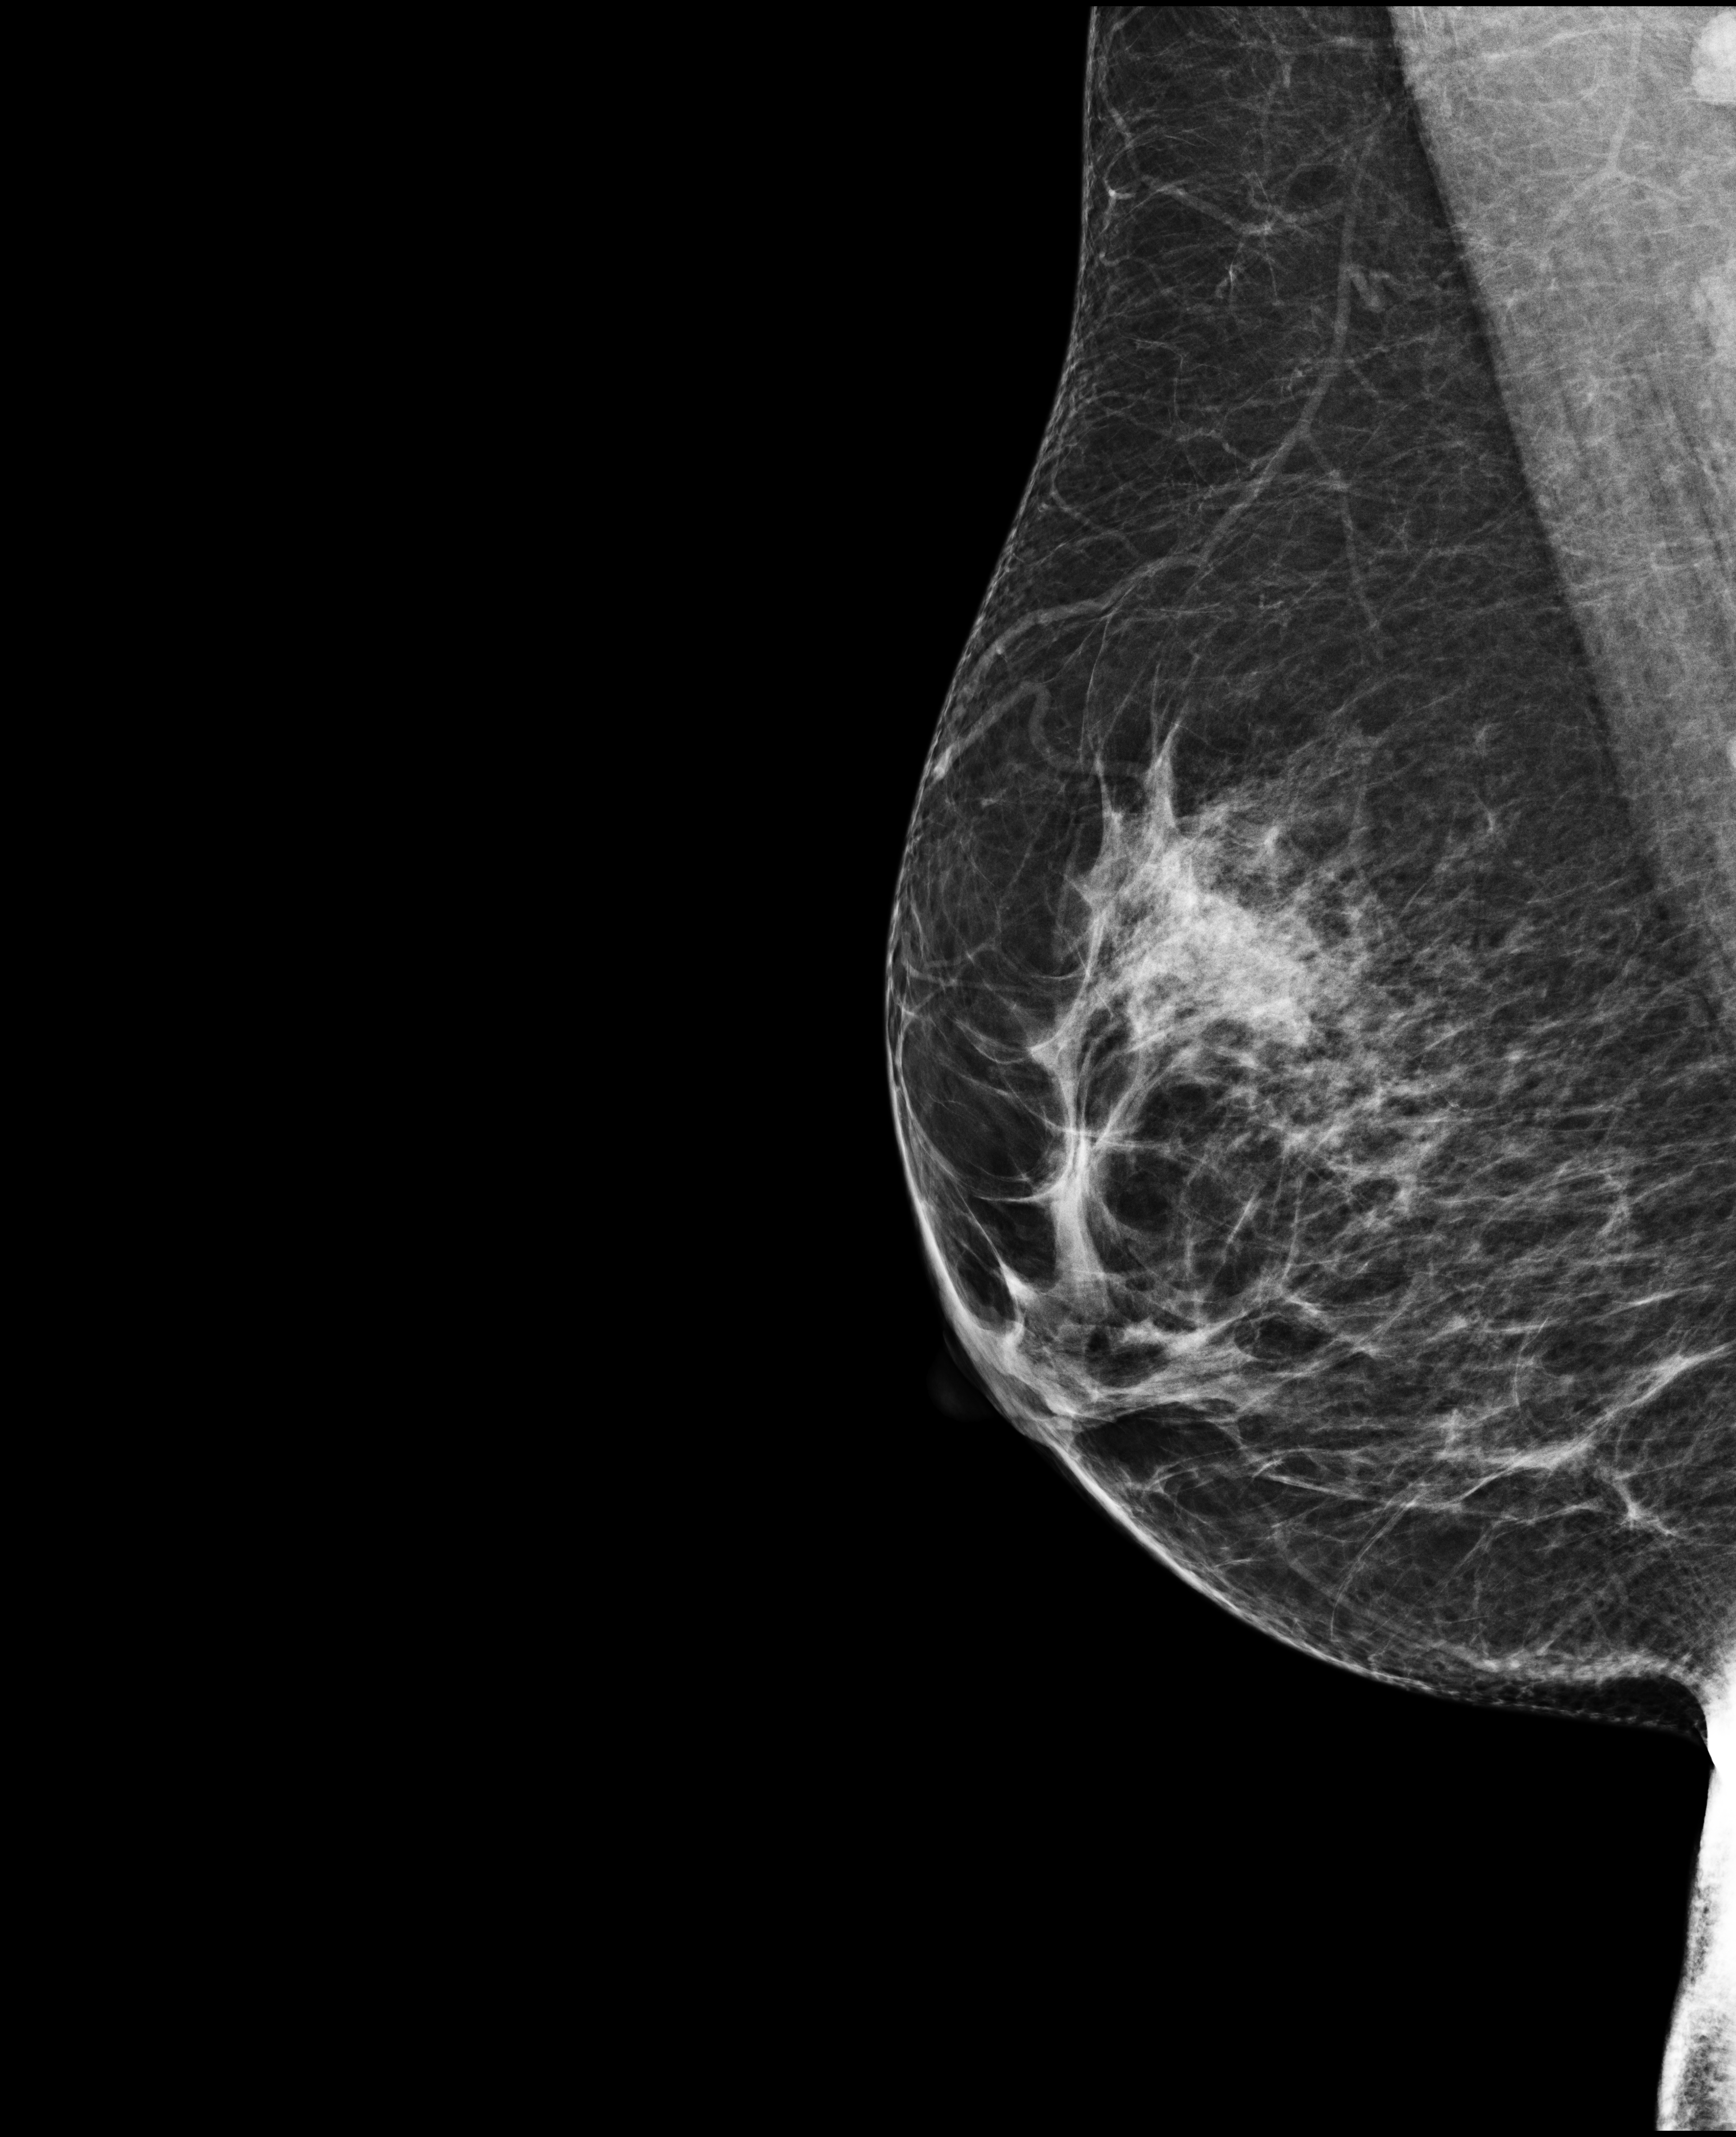
Full-field digital mammogram (FFDM); right breast; MLO view; screening examination; system: Selenia Dimensions. Female patient, age 56 years.
BI-RADS breast density category at the screening exam (both breasts, scale 1–4): 3.